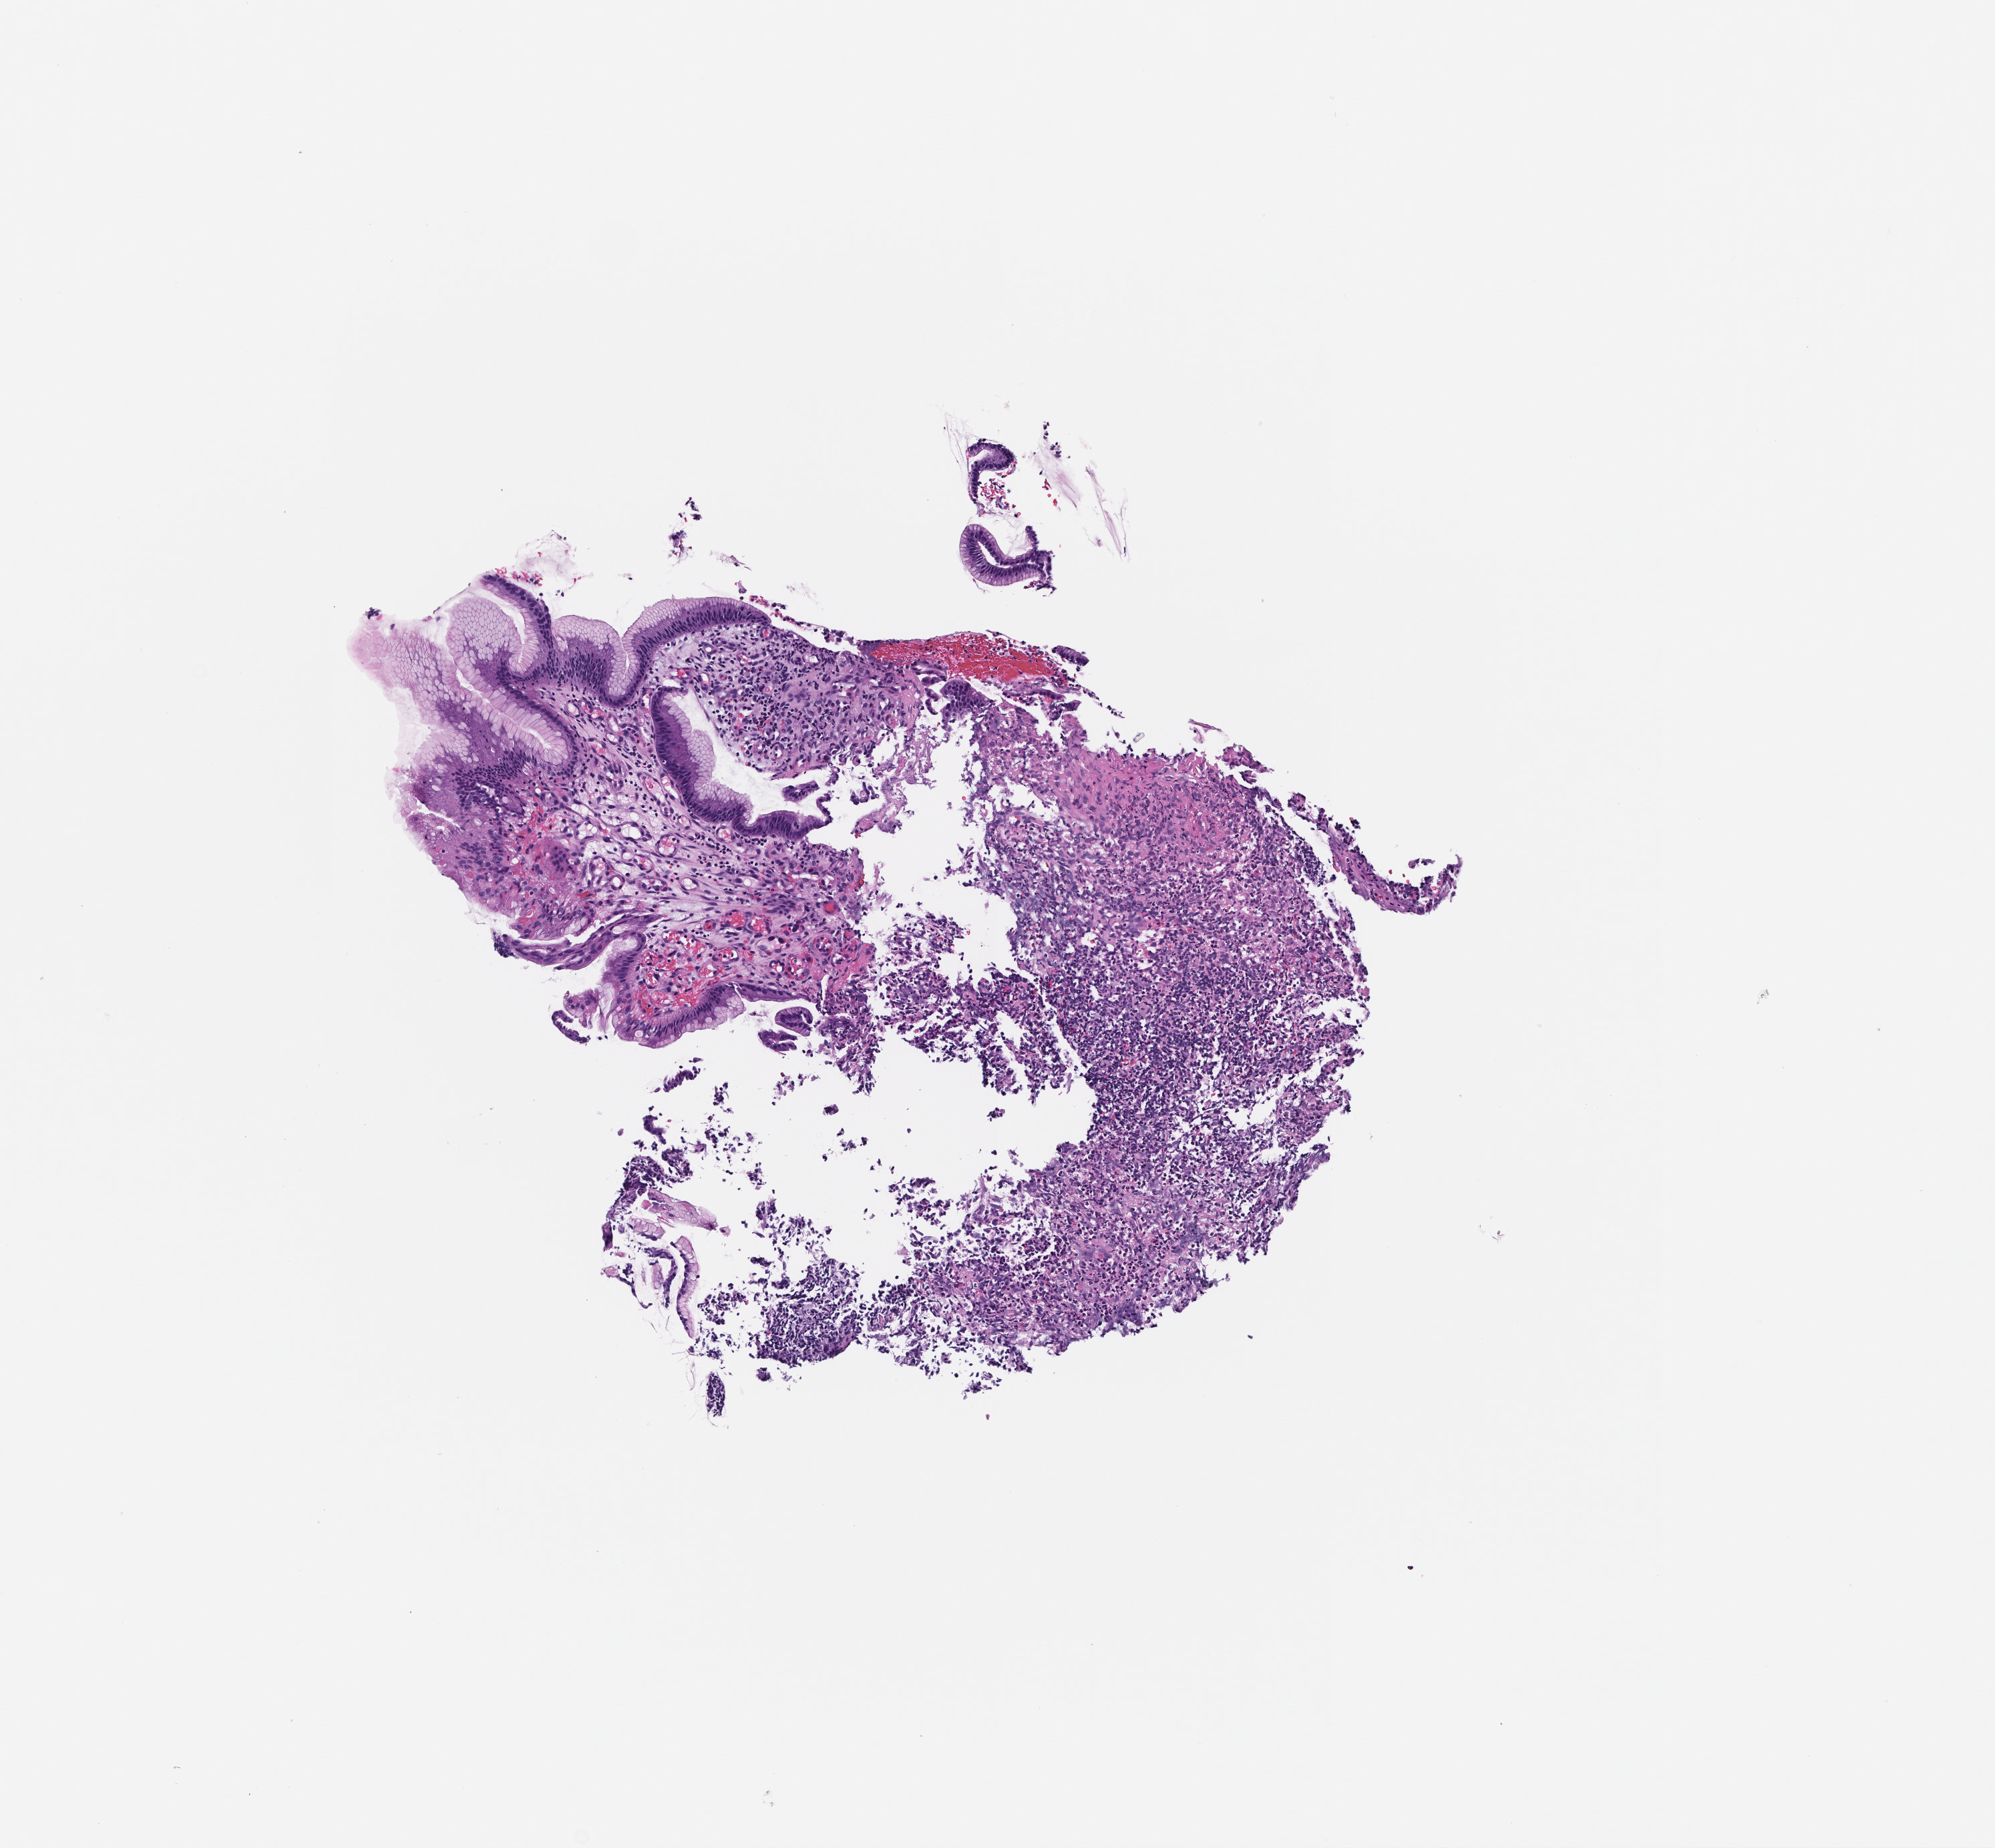
H&E whole-slide image, a low-resolution overview of the entire scanned area, about 3.0 x 2.8 mm; formalin-fixed, paraffin-embedded (FFPE) tissue; tissue site: stomach; specimen time point: archival tissue. Patient: female.
* this section: primary tumour tissue
* diagnosis: Adenocarcinoma of the Gastroesophageal Junction